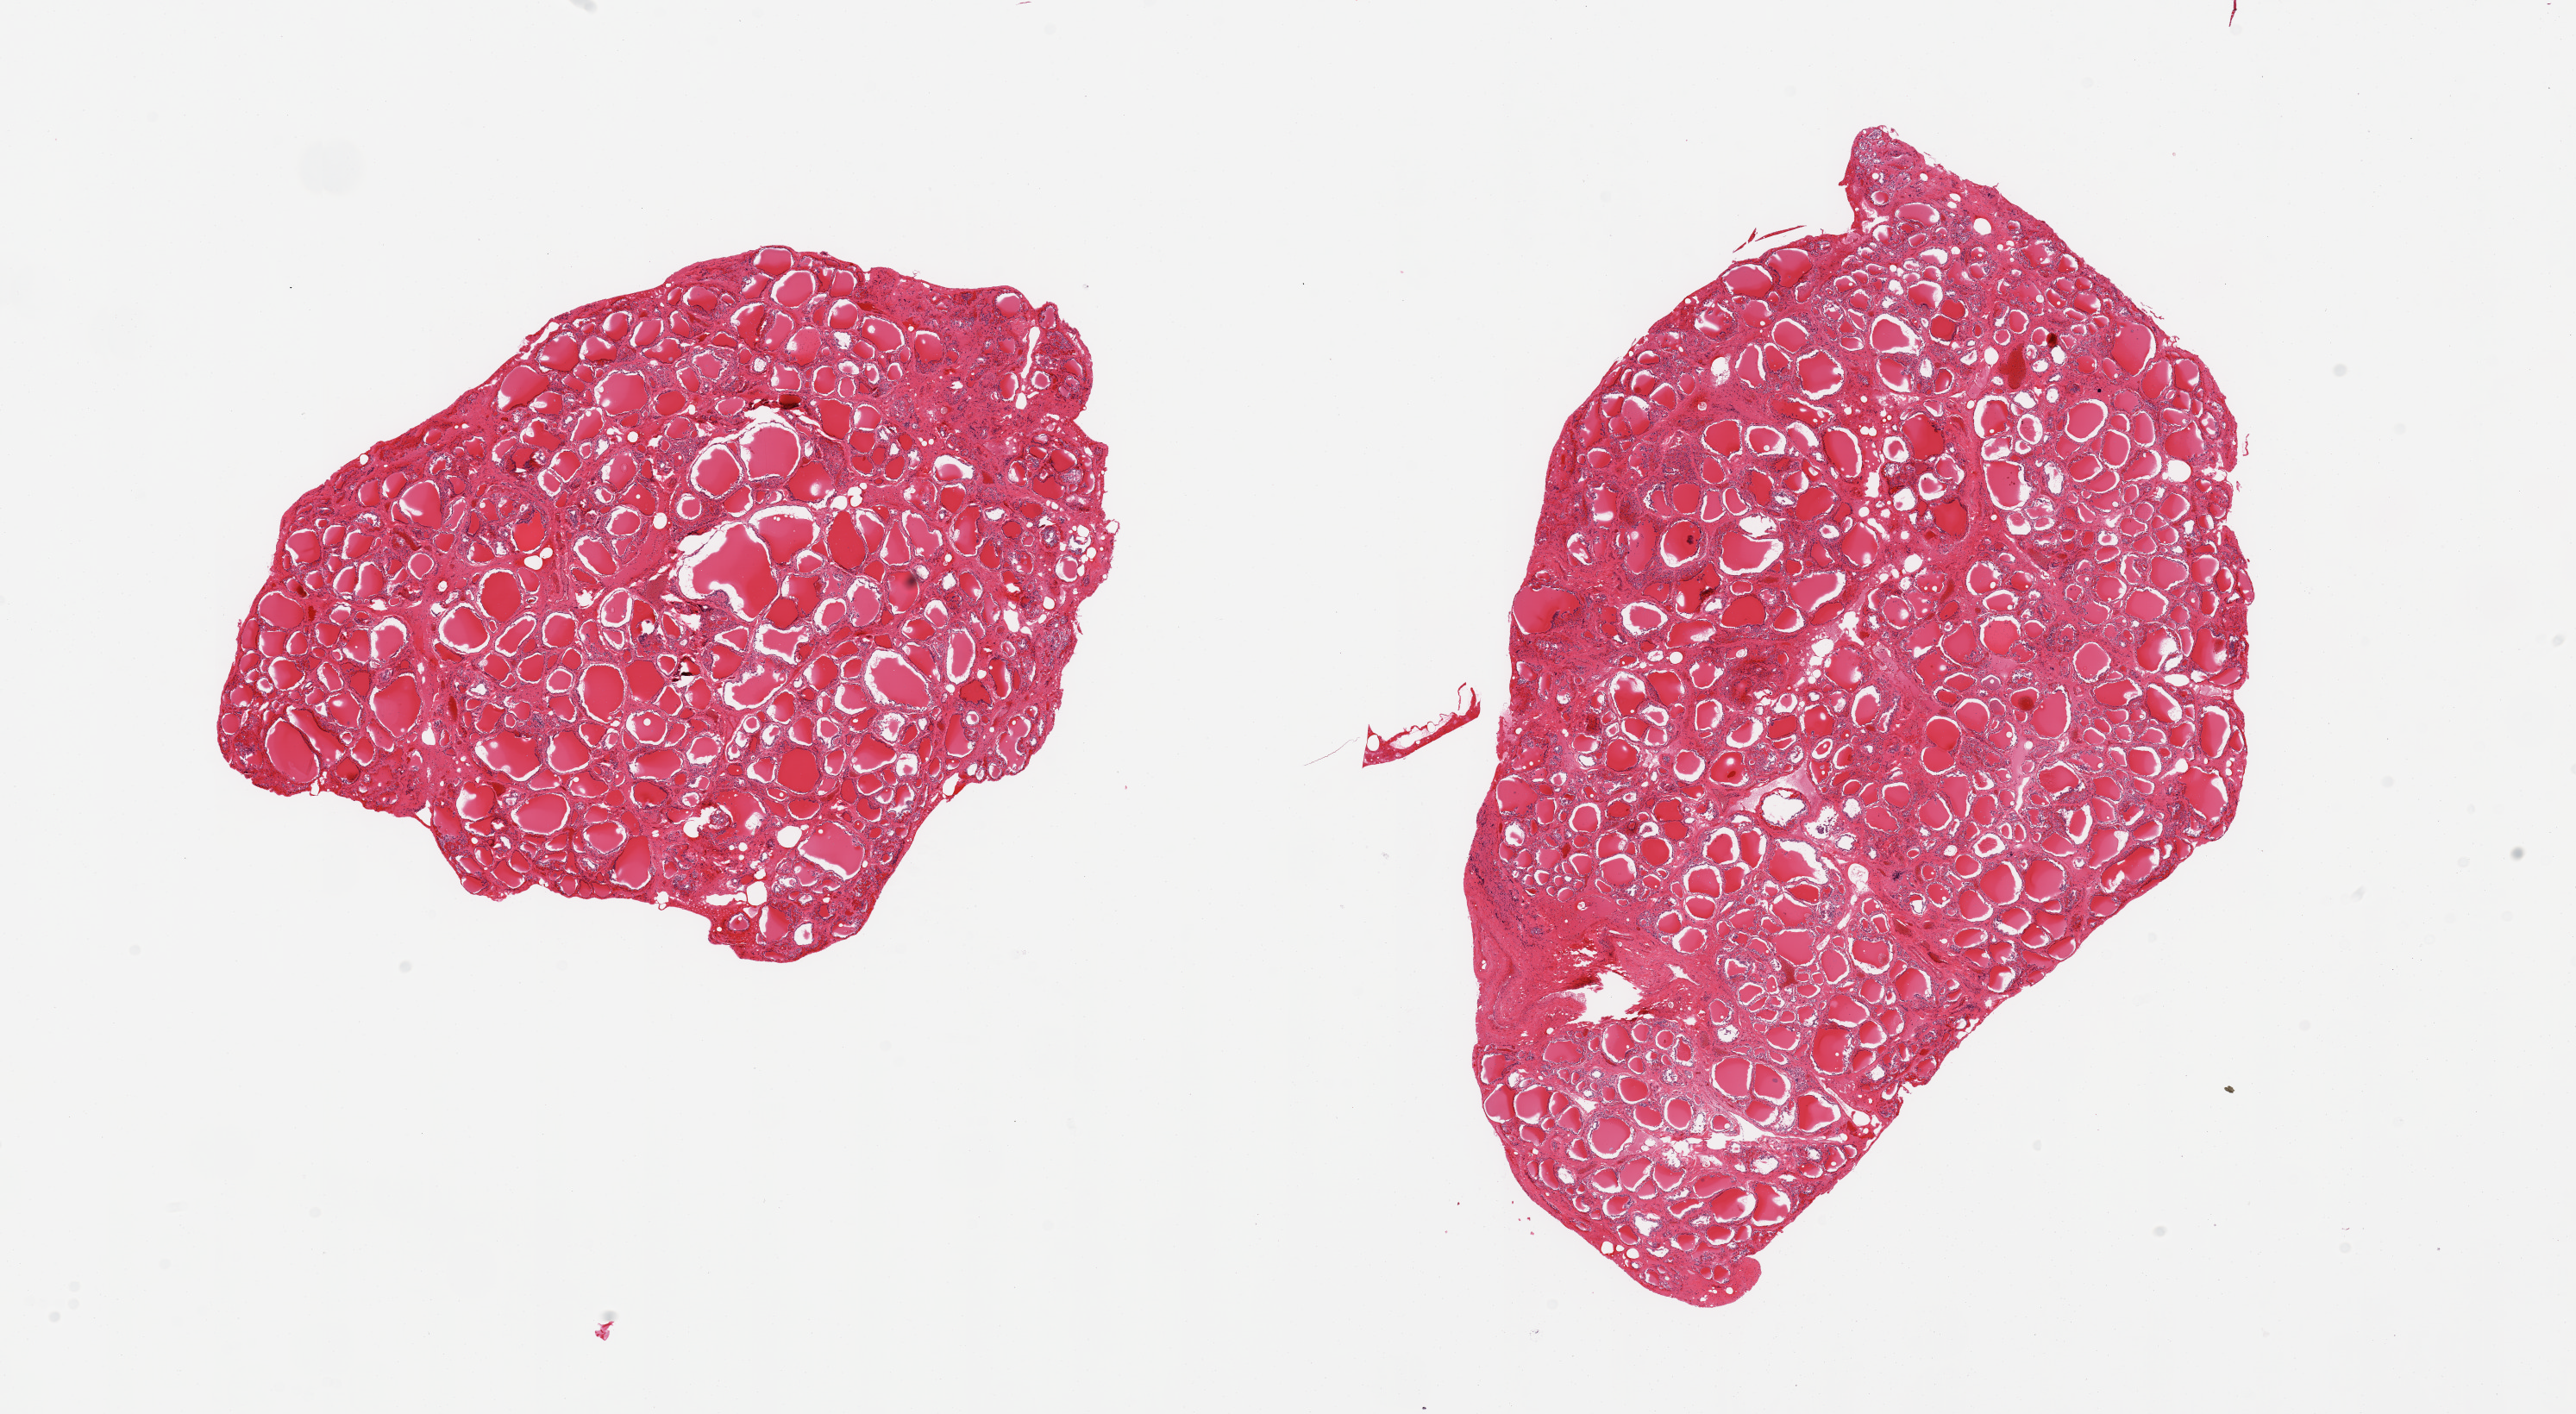
Digitized hematoxylin and eosin (H&E)-stained section, low-resolution overview of the scanned area, about 23.6 x 13.0 mm, PAXgene-fixed paraffin-embedded (PFPE) section, target tissue: thyroid, donor tissue sample. Donor: male.
Pathologist's review note for this sample: 2 pieces.